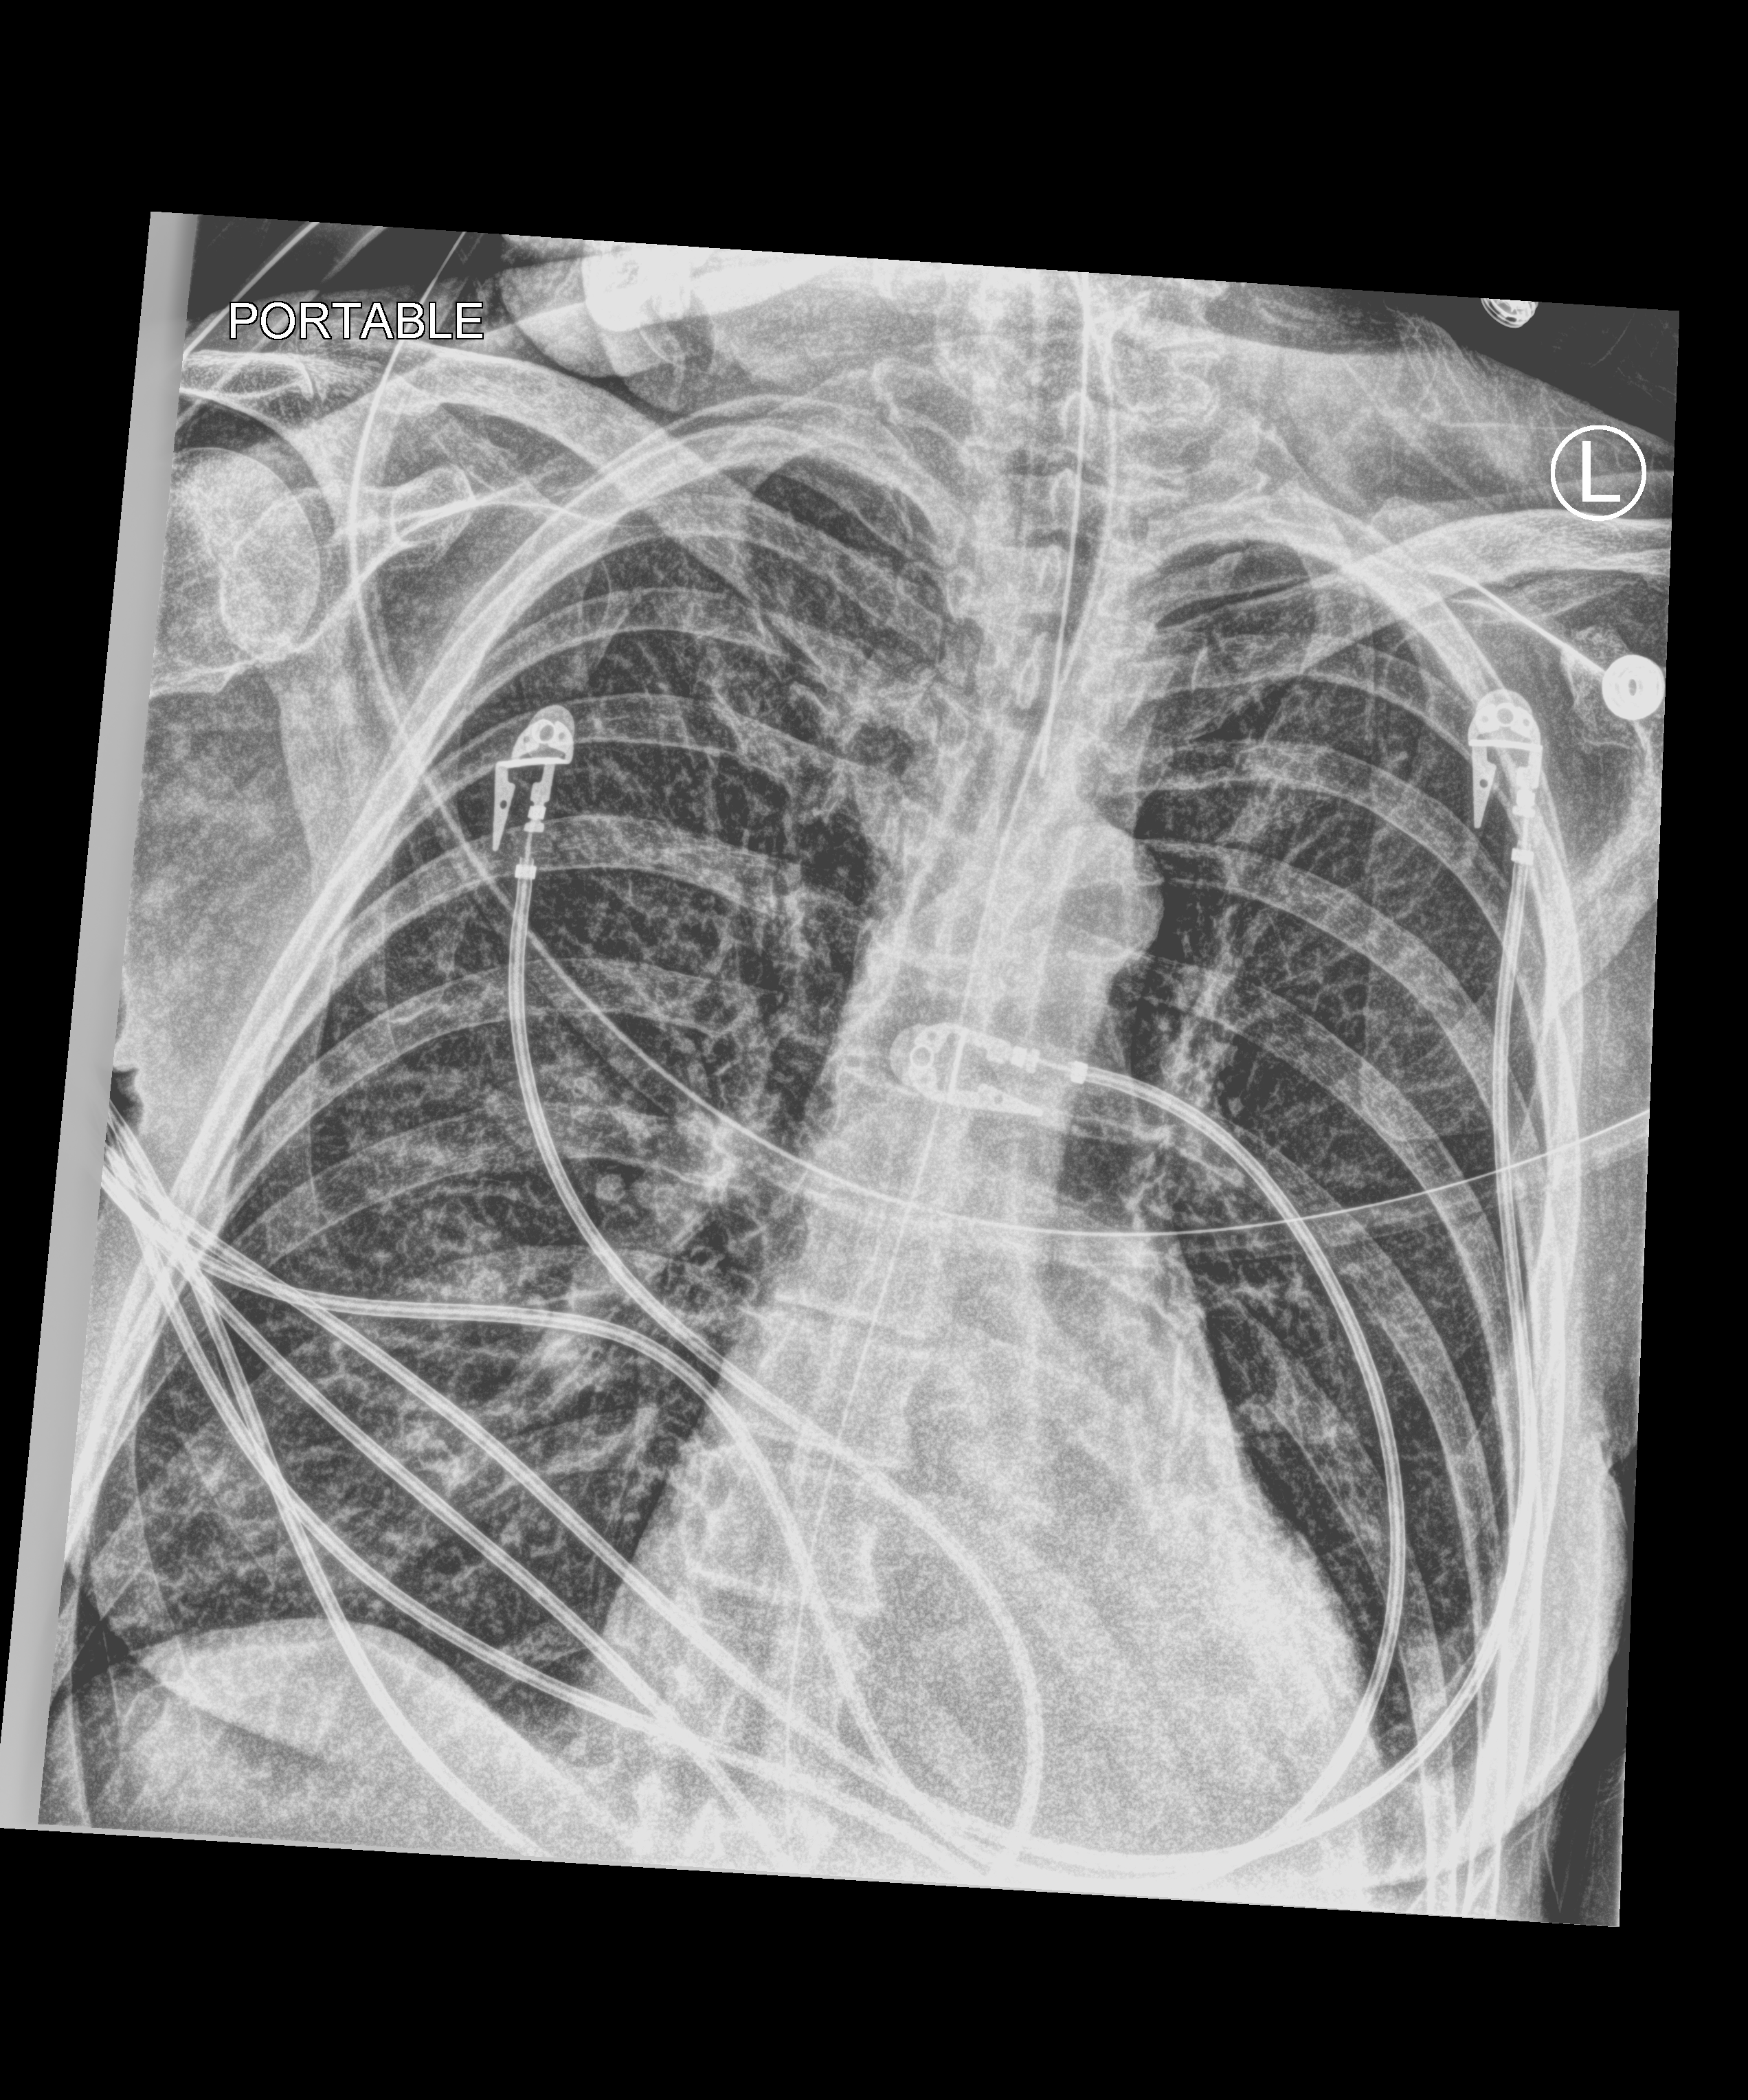
Chest X-ray (portable), anteroposterior (AP) projection. Female patient hospitalised with COVID-19, age 60–74 years.
Hospital-stay facts (about this admission, not read from this image; timing relative to this image not recorded): mechanically ventilated during this hospital stay: yes; admitted to intensive care during this hospital stay: yes; length of hospital stay: 38 days.